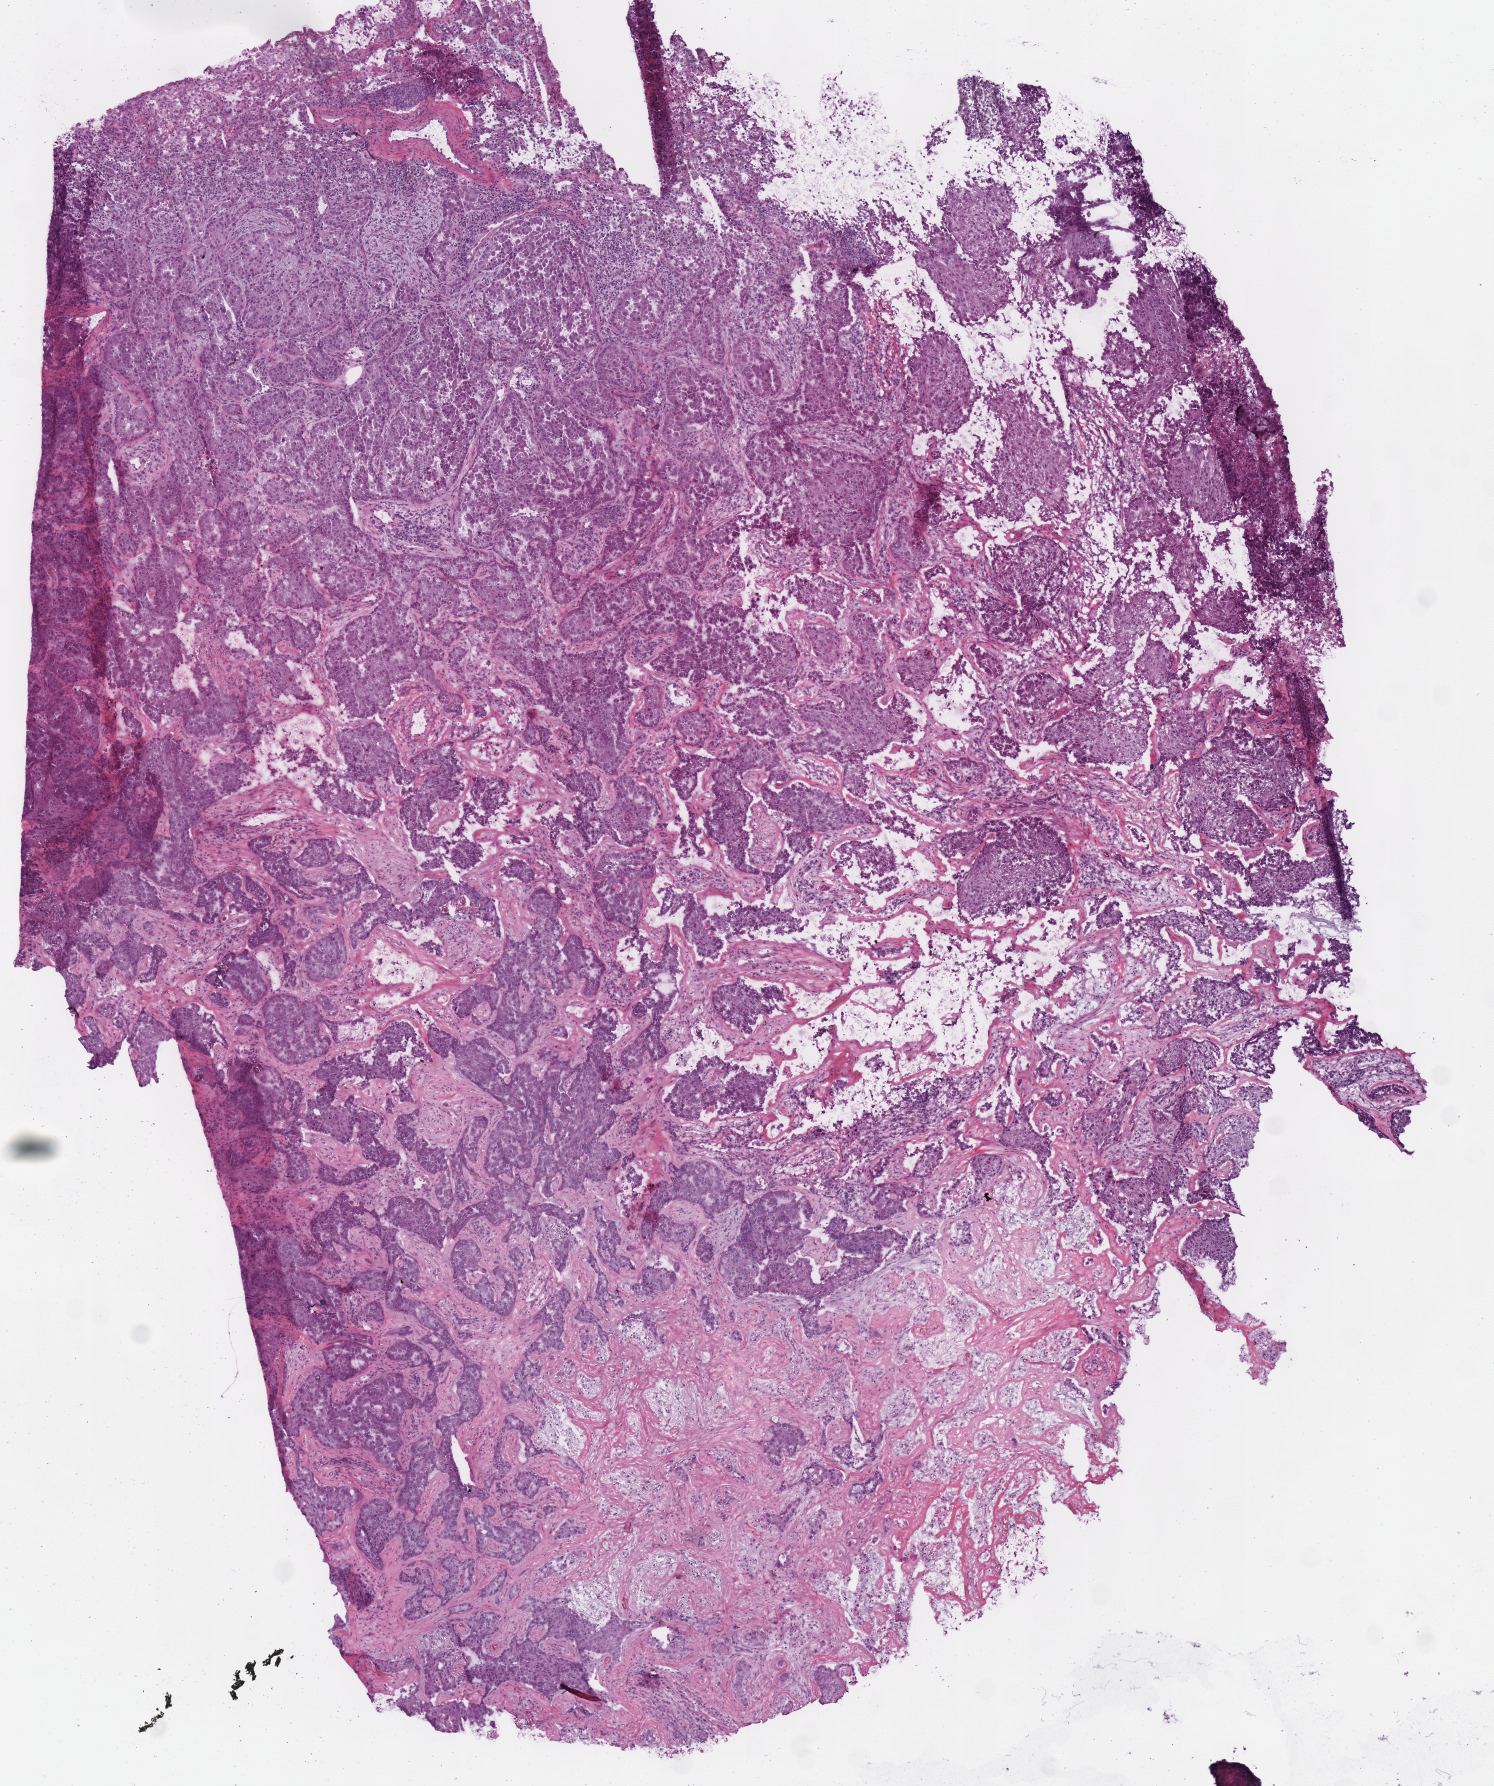
Digitized H&E tissue section (whole slide) — whole scanned area (about 5.9 x 7.0 mm) shown as a low-resolution overview. Frozen section from the top of the tissue portion. Sample: primary tumour, lung. Patient: female, age at initial diagnosis 54 years. Composition of this section per pathologist review: tumour cells 95%, tumour nuclei 80%, normal cells 0%, stromal cells 5%, necrosis 0%. Inflammatory infiltration, as recorded: lymphocyte infiltration 10%, monocyte infiltration 0%, neutrophil infiltration 0%.
AJCC pathologic stage: IB. Pathologic diagnosis: Adenocarcinoma, NOS (upper lobe, lung). TNM: T2a N0 M0.